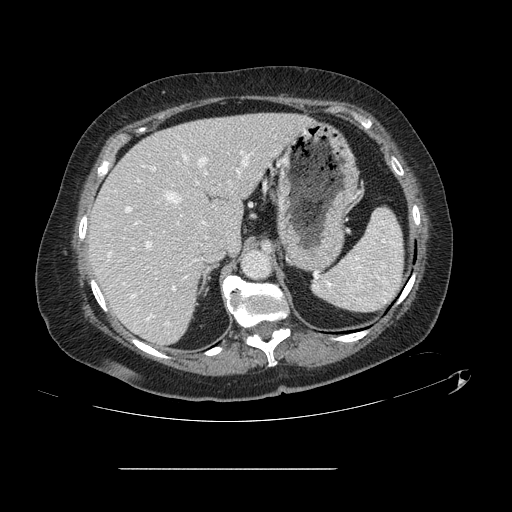
Contrast-enhanced abdominal CT, one axial slice. Position 92 of 148 along the scan axis. 120 kVp. Intravenous contrast given. Soft-tissue window (W 400 / L 40 HU). 512 × 512 image matrix, field of view 439 × 439 mm. Female patient, age 75 years. From the clinical record (not read from this slice): diagnosis: colorectal cancer liver metastases, imaged before liver resection; multiple liver metastases: no; largest metastasis: 2.4 cm; disease in both lobes: no.
Annotated regions visible in this slice (manually delineated by an expert):
- hepatic veins: bounding box (x1, y1, x2, y2) in pixels: (132, 157, 241, 320)
- liver: (90, 114, 308, 345)
- planned liver remnant (the part of the liver to remain after resection): (90, 114, 308, 345)
- portal vein (with intrahepatic branches): (126, 150, 253, 290)